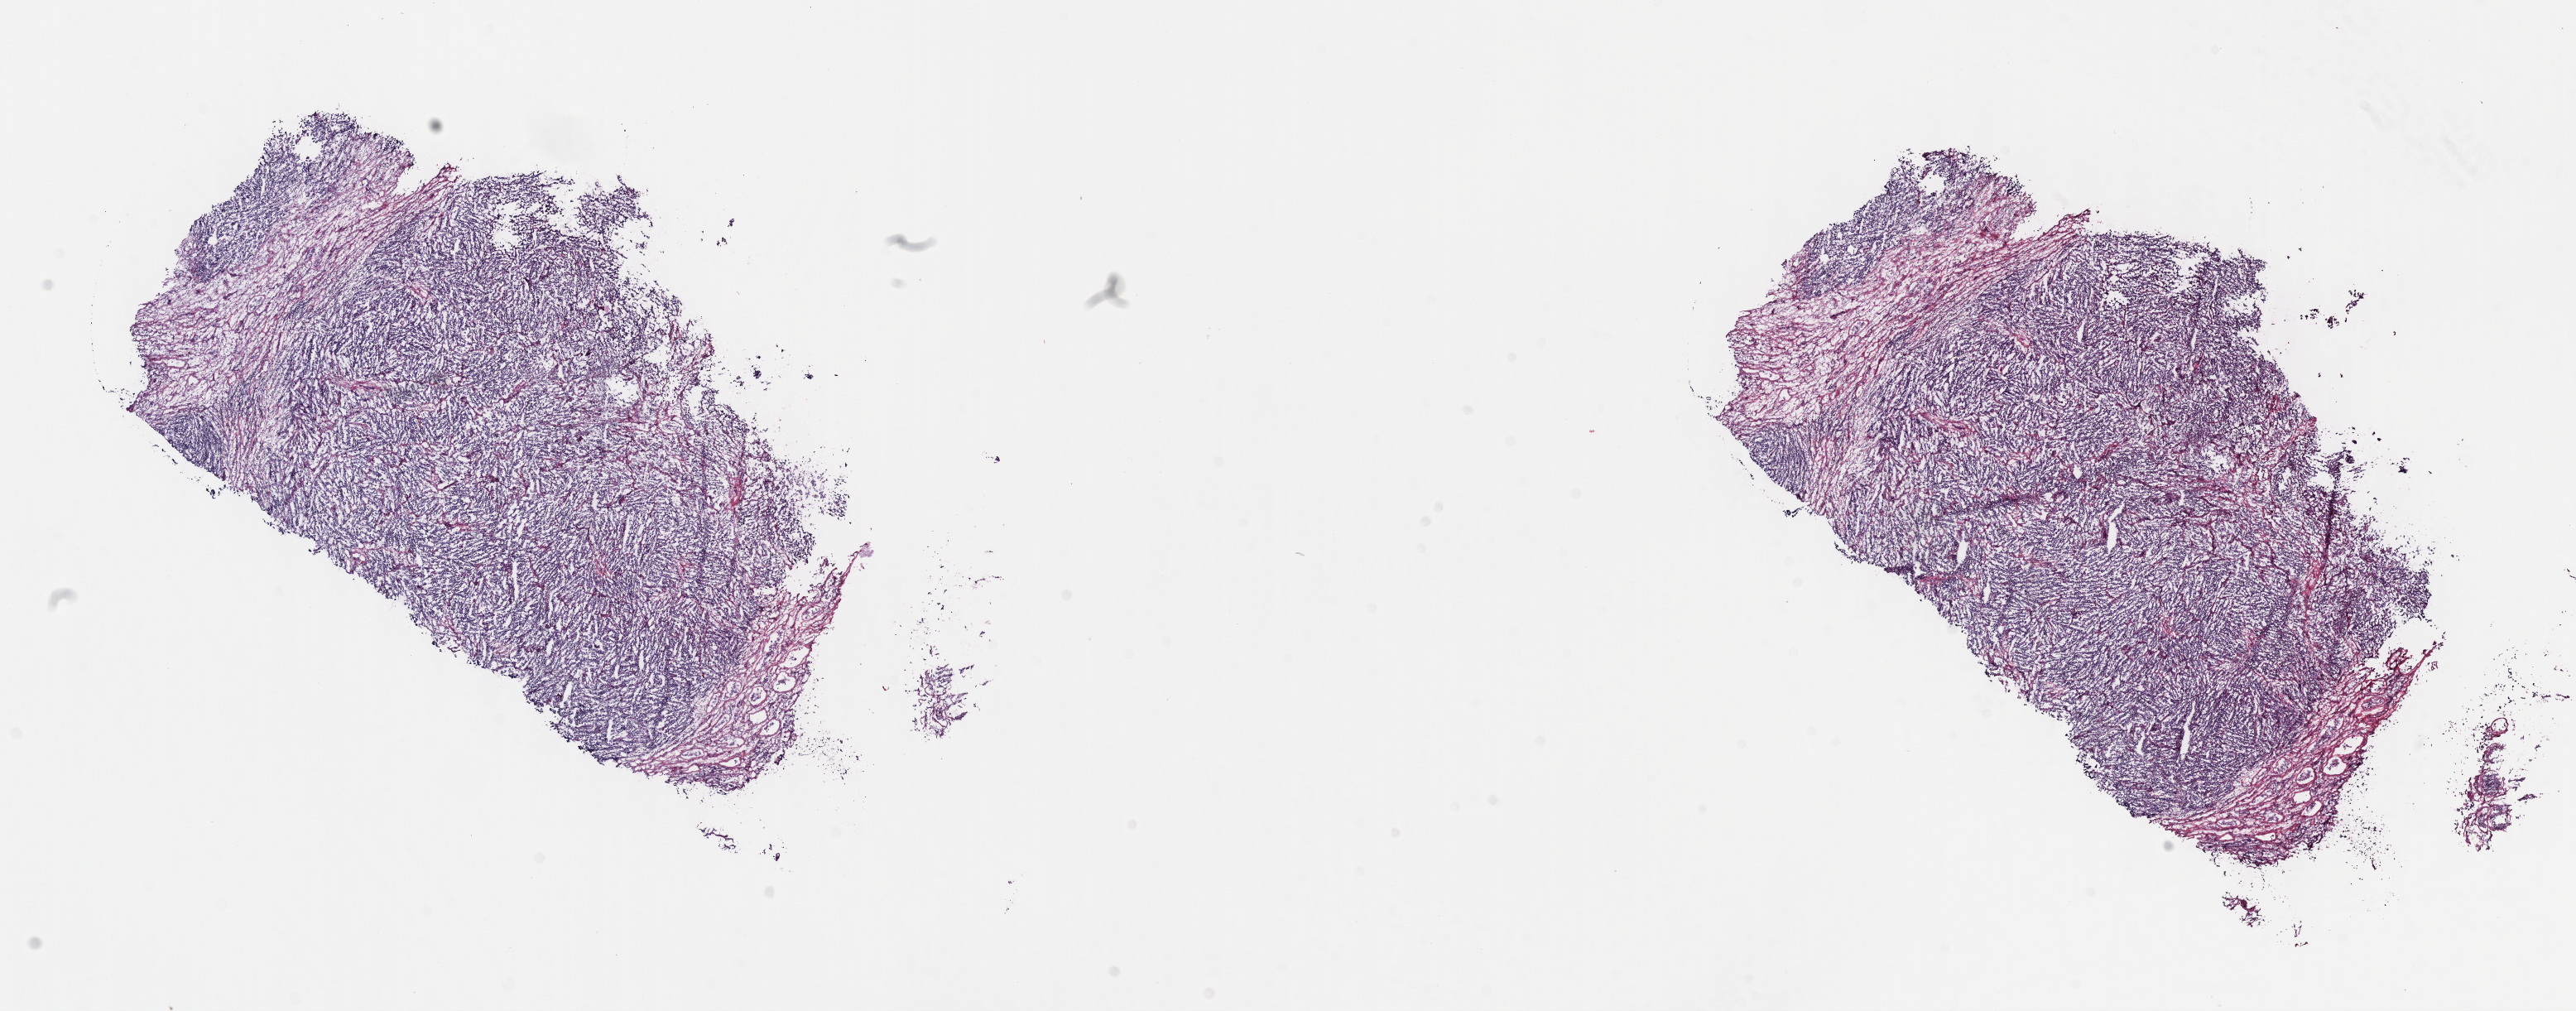
H&E whole-slide image — low-resolution overview of the scanned area, about 25.2 x 9.9 mm. Frozen section from the top of the tissue portion. Testis, primary tumour sample. Male, age 40 years at initial diagnosis.
Diagnosis: Seminoma, NOS.